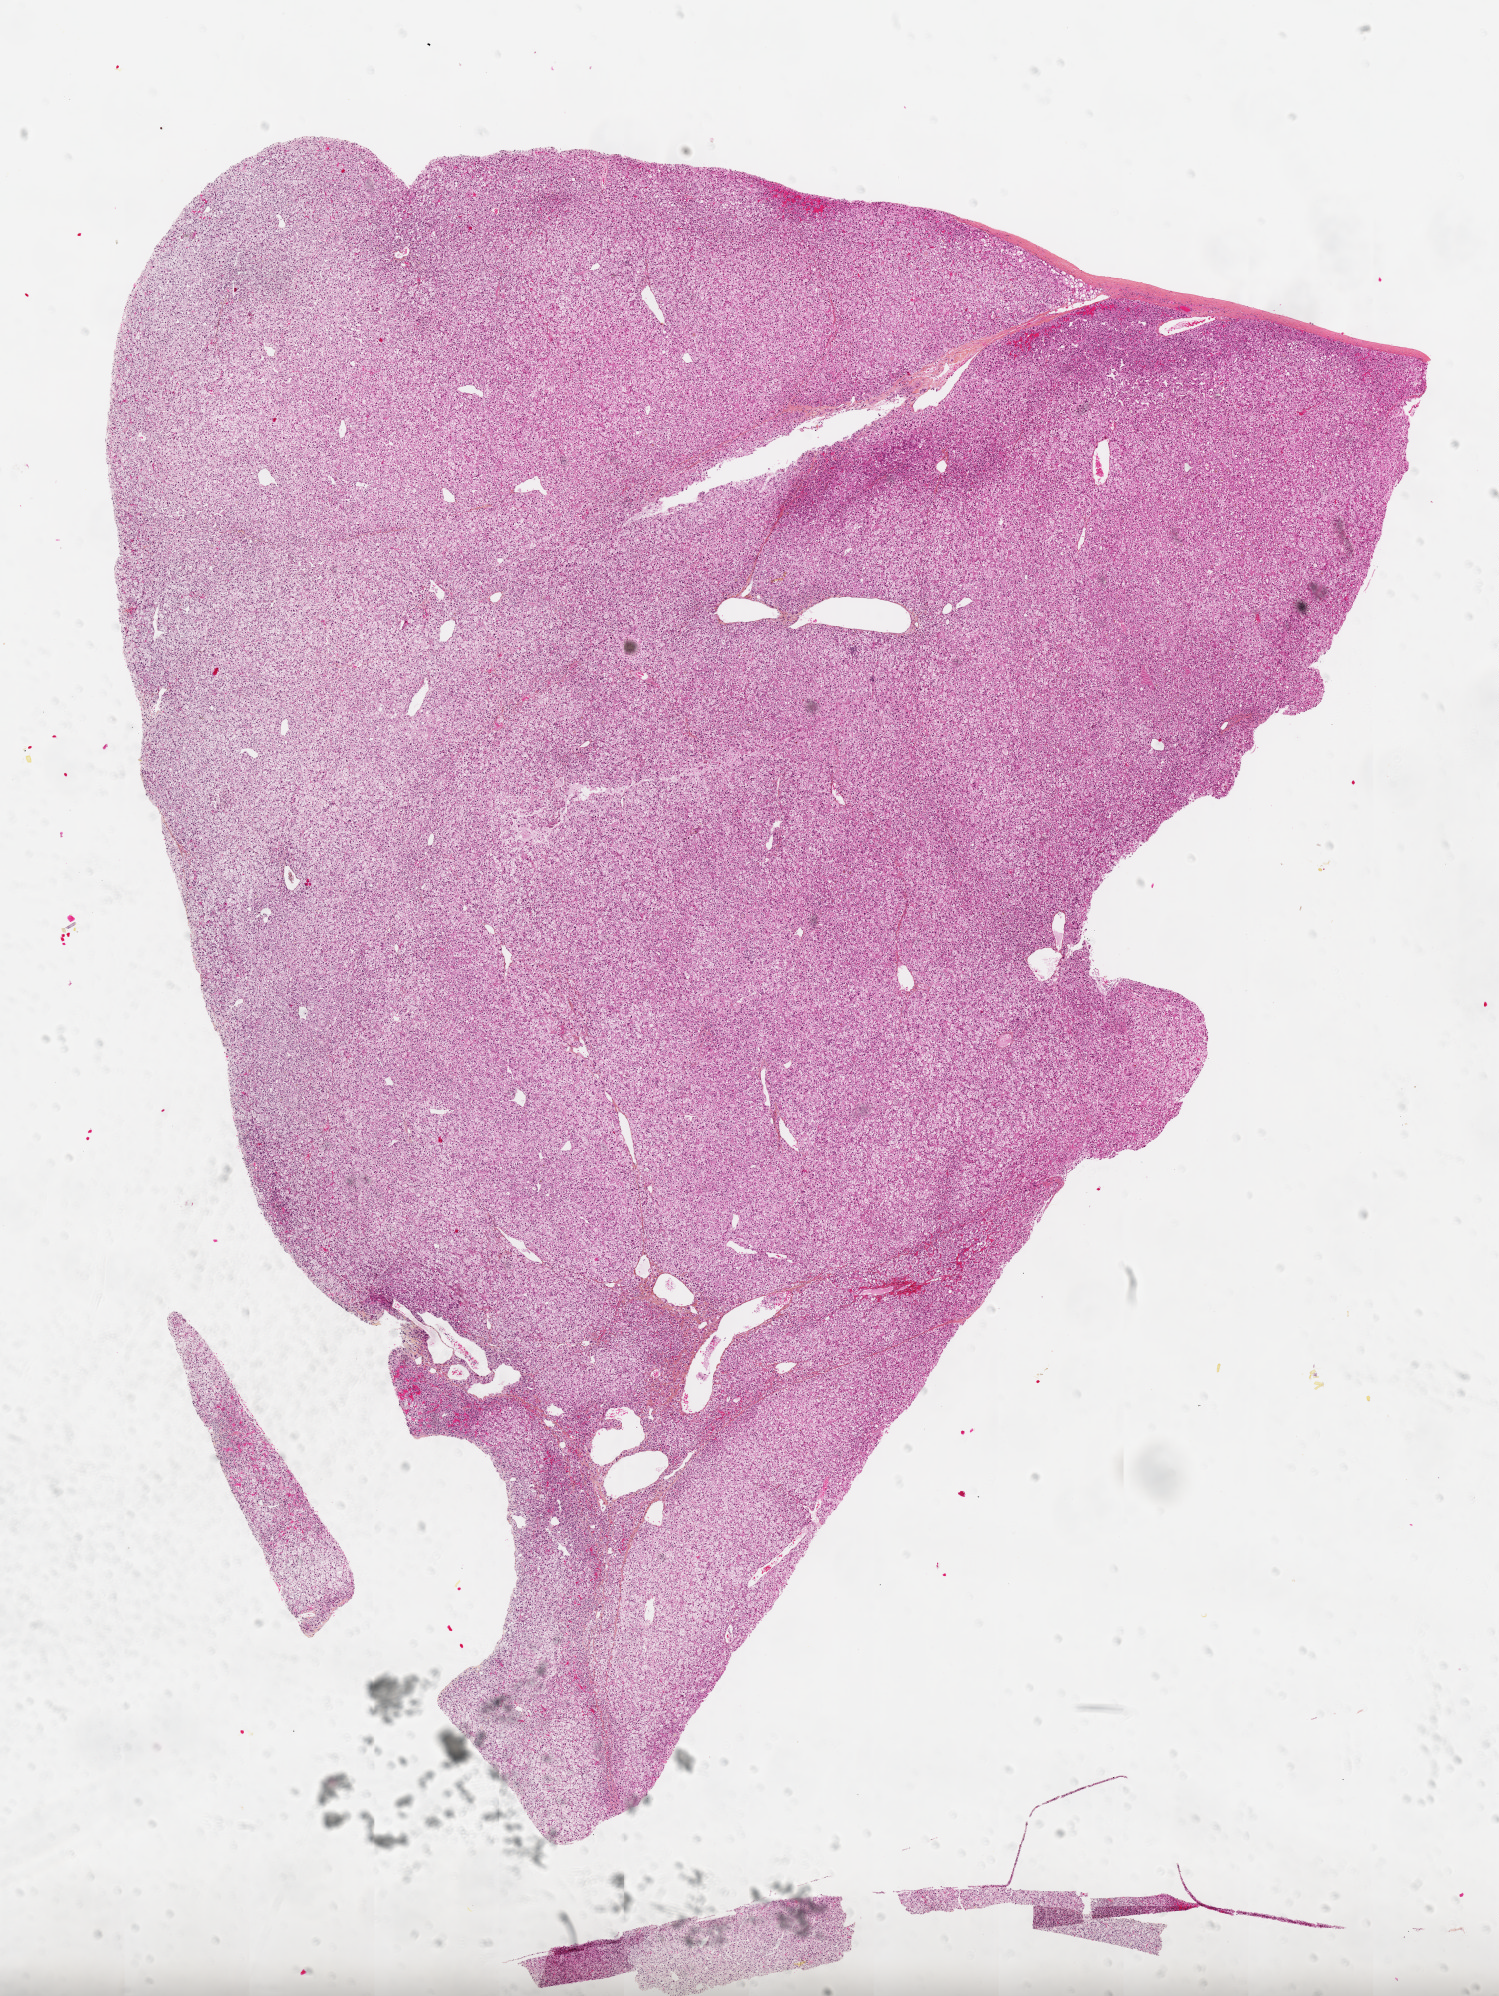
Digitized Hematoxylin and eosin (H&E) stained tissue section (whole slide) — low-resolution overview of the scanned area, about 12.0 x 16.0 mm (slide scanned at 20x). Formalin-fixed paraffin-embedded (FFPE) diagnostic section. Primary tumour sample from the liver. Patient sex: female.
Histologic diagnosis: Hepatocellular carcinoma, clear cell type.